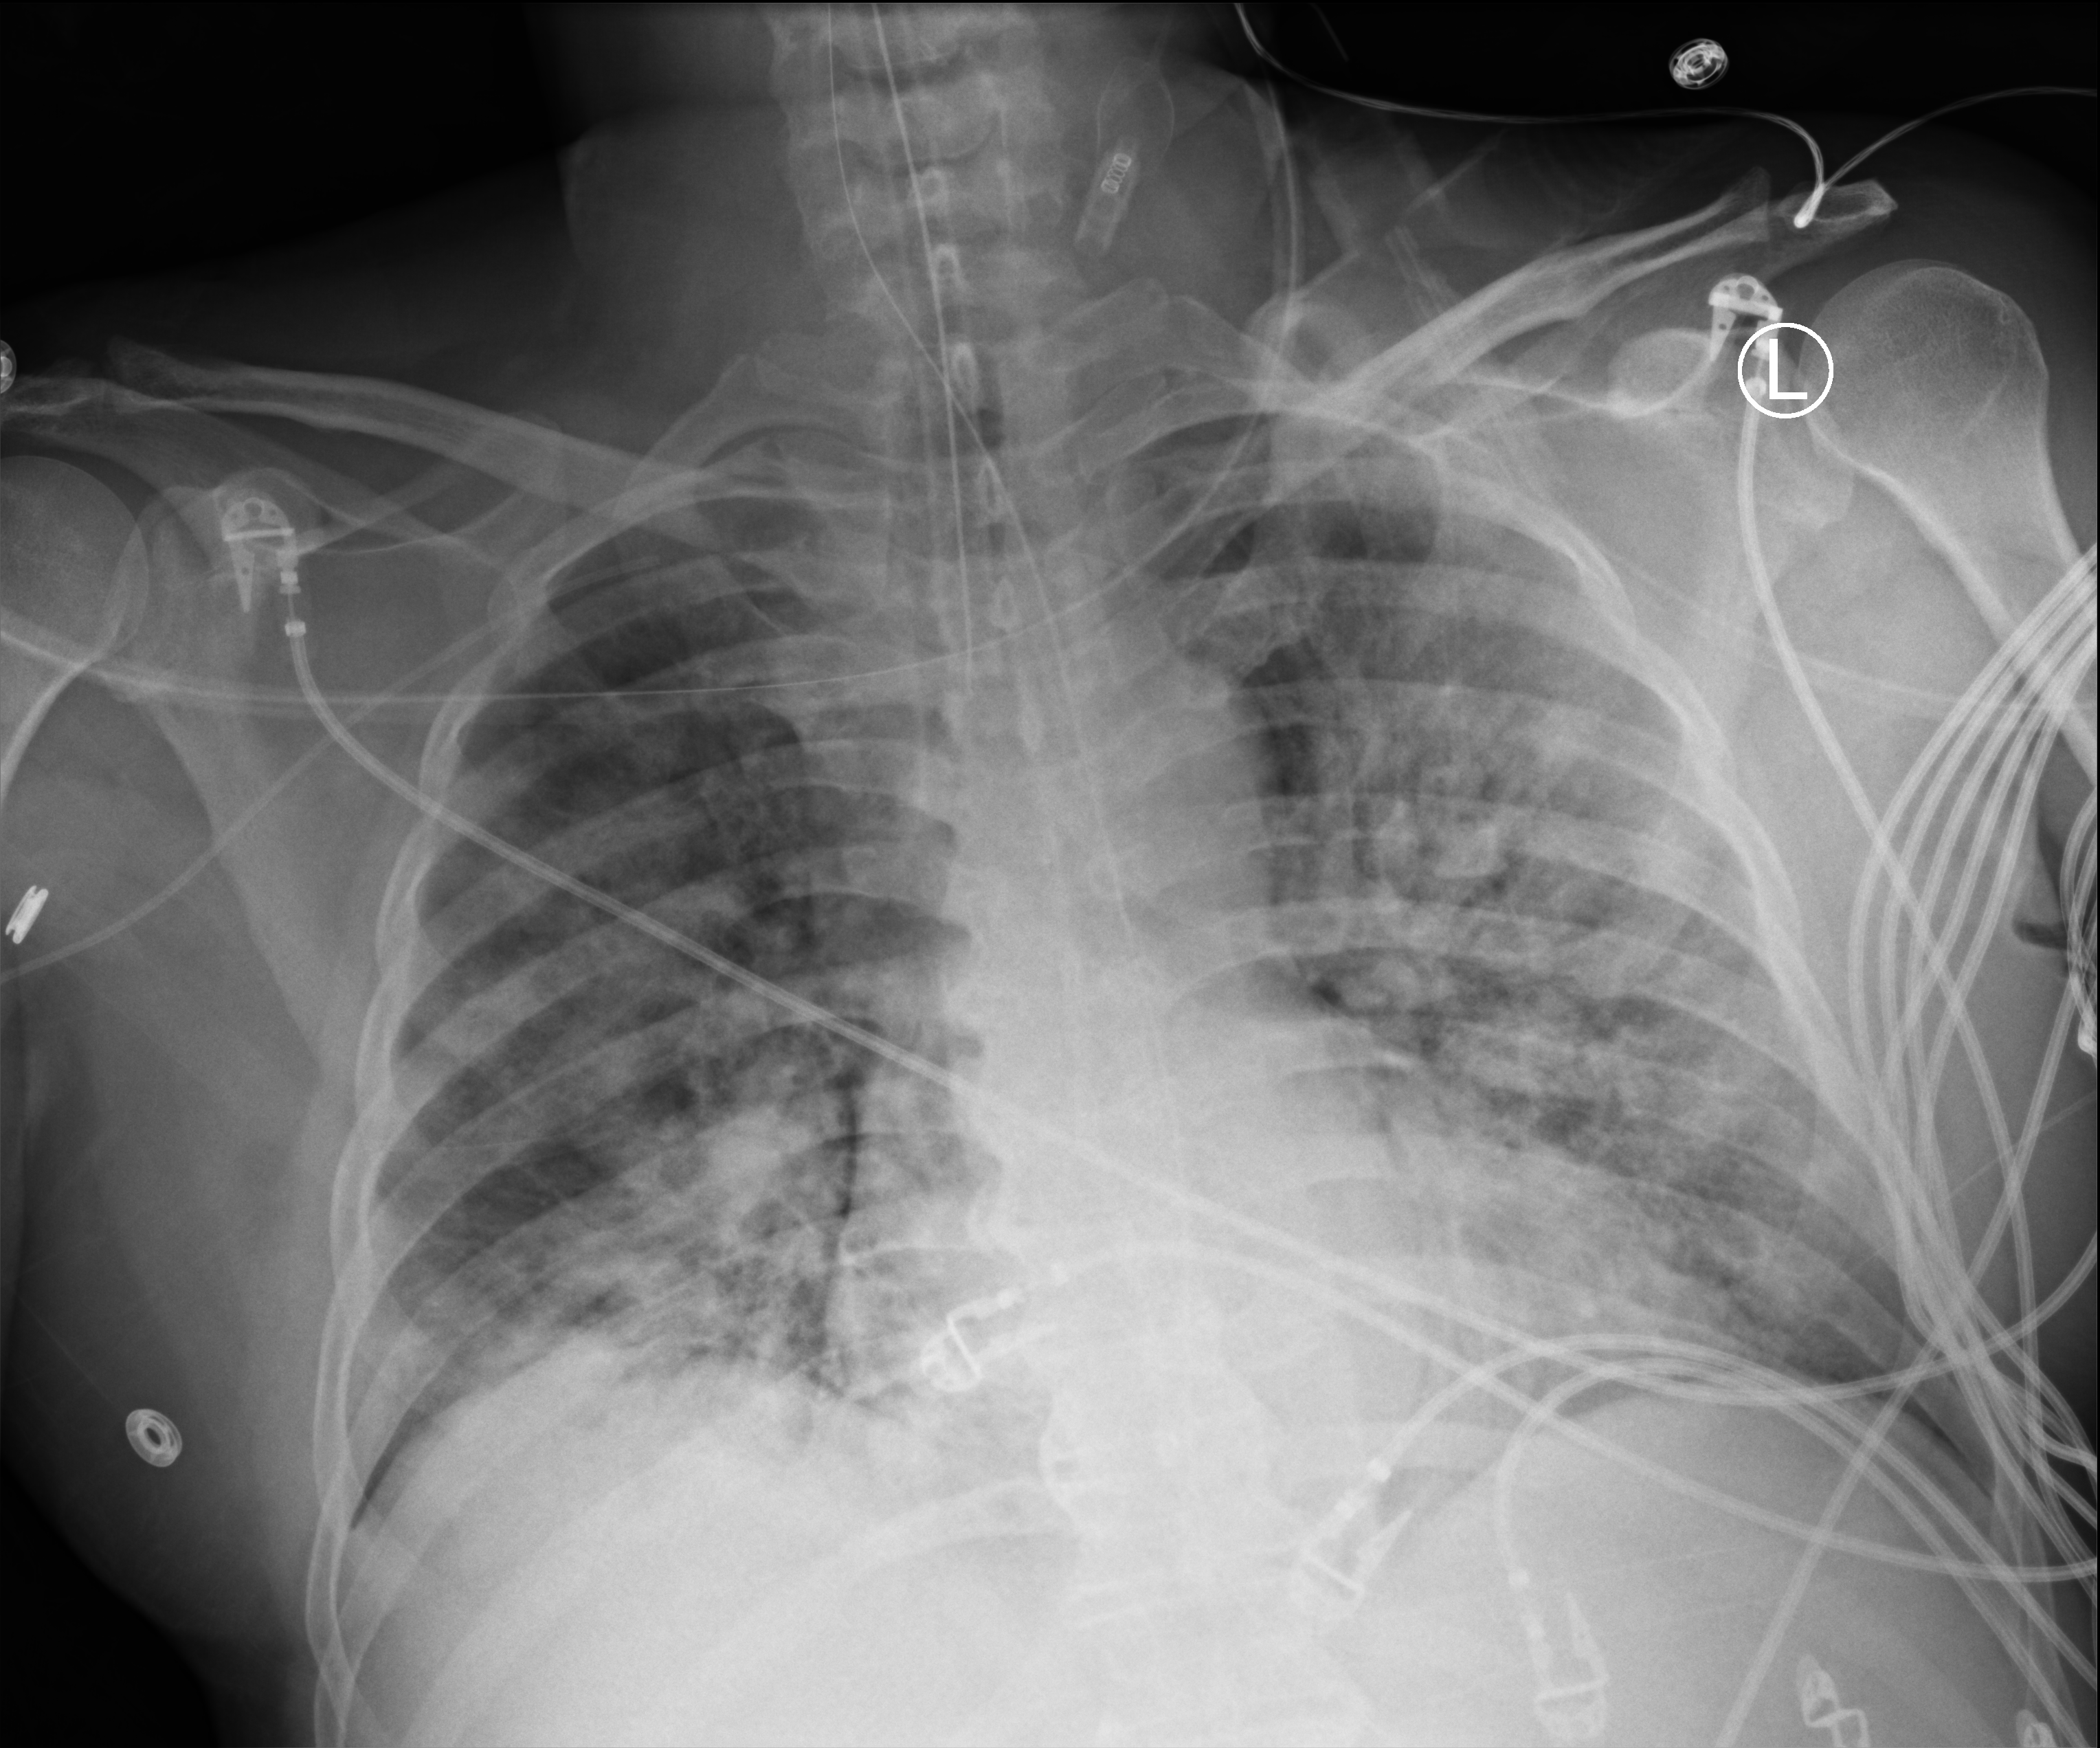
Chest X-ray (portable), anteroposterior (AP) projection. Patient hospitalised with COVID-19; male, aged 18–59 years.
Hospital-stay facts (about this admission, not read from this image; timing relative to this image not recorded): admitted to intensive care during this hospital stay: yes; mechanically ventilated during this hospital stay: yes.